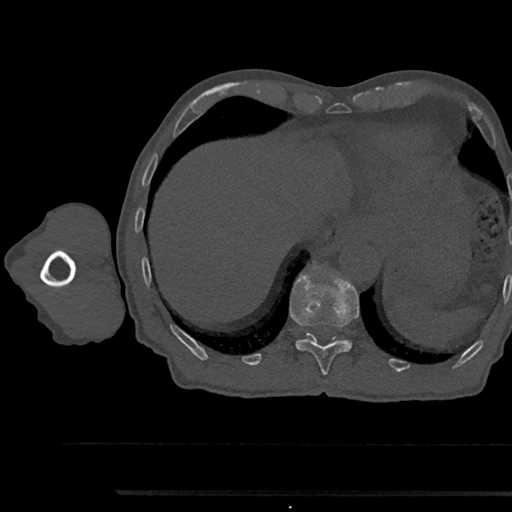
CT including the spine, one axial slice; position 773 of 797 along the scan axis; 120 kVp; bone window (W 1800 / L 400 HU); 0.5 mm slice thickness; 512 × 512 image matrix, field of view 367 × 367 mm. Male patient, age 79 years. From the clinical record (not read from this slice): primary cancer: prostate.
Outlined on this slice (semi-automatically segmented with operator editing):
- T11 vertebra: bounding box <290,266,359,377> (left, top, right, bottom; pixels)